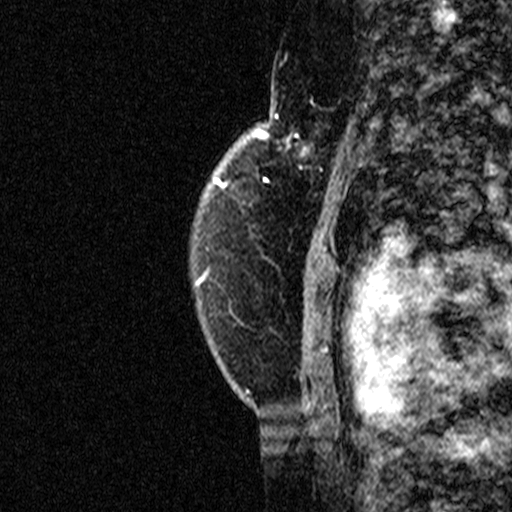
Breast MRI (dynamic contrast-enhanced), one sagittal slice; dynamic contrast-enhanced study with each time point stored as its own series, time point 2 of 3 at this slice position (early post-contrast, ordered by acquisition time); 1.5 T; TE 4.5 ms, TR 11 ms; 3 mm slice thickness; 512 × 512 image matrix, field of view 200 × 200 mm. Patient: female, 49 years. From the clinical record (not read from this slice): setting: breast cancer imaged before/during neoadjuvant chemotherapy; receptor status: triple-negative.
Outlined on this slice (semi-automatic segmentation, software-assisted and operator-edited):
- analysis volume of interest (the breast-tissue region the enhancement analysis was run in; not a lesion): bounding box (x1, y1, x2, y2) in pixels: (254, 112, 347, 207)
- tumour enhancement mask (voxels above the 90 % enhancement threshold inside the analysis volume of interest): (254, 114, 347, 205)